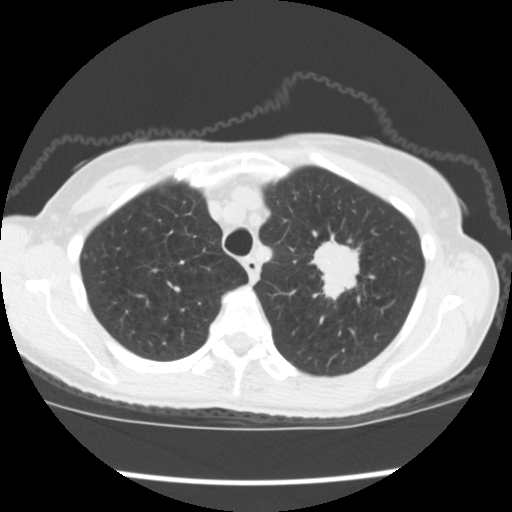
Chest CT (low-dose screening protocol), one axial image, baseline screening round, lung window (W 1500 / L -600 HU), slice 31 of 176 in the series. Female participant, aged 67 years at enrolment. Former smoker at enrolment.
Expert reader's lesion annotation, bounding box [x1, y1, x2, y2] px = [304, 235, 376, 310]. Reader record for this screening exam (exam-level; its link to the box is not recorded): non-calcified nodule or mass ≥4 mm, left upper lobe, 34 × 32 mm, spiculated (stellate) margins, soft tissue attenuation, pre-existing on the prior screen: no. Later outcome: lung cancer diagnosed 17 days after this screen — small cell carcinoma, NOS, left upper lobe, stage IIIA (AJCC 6th edition), 40 mm at pathology.